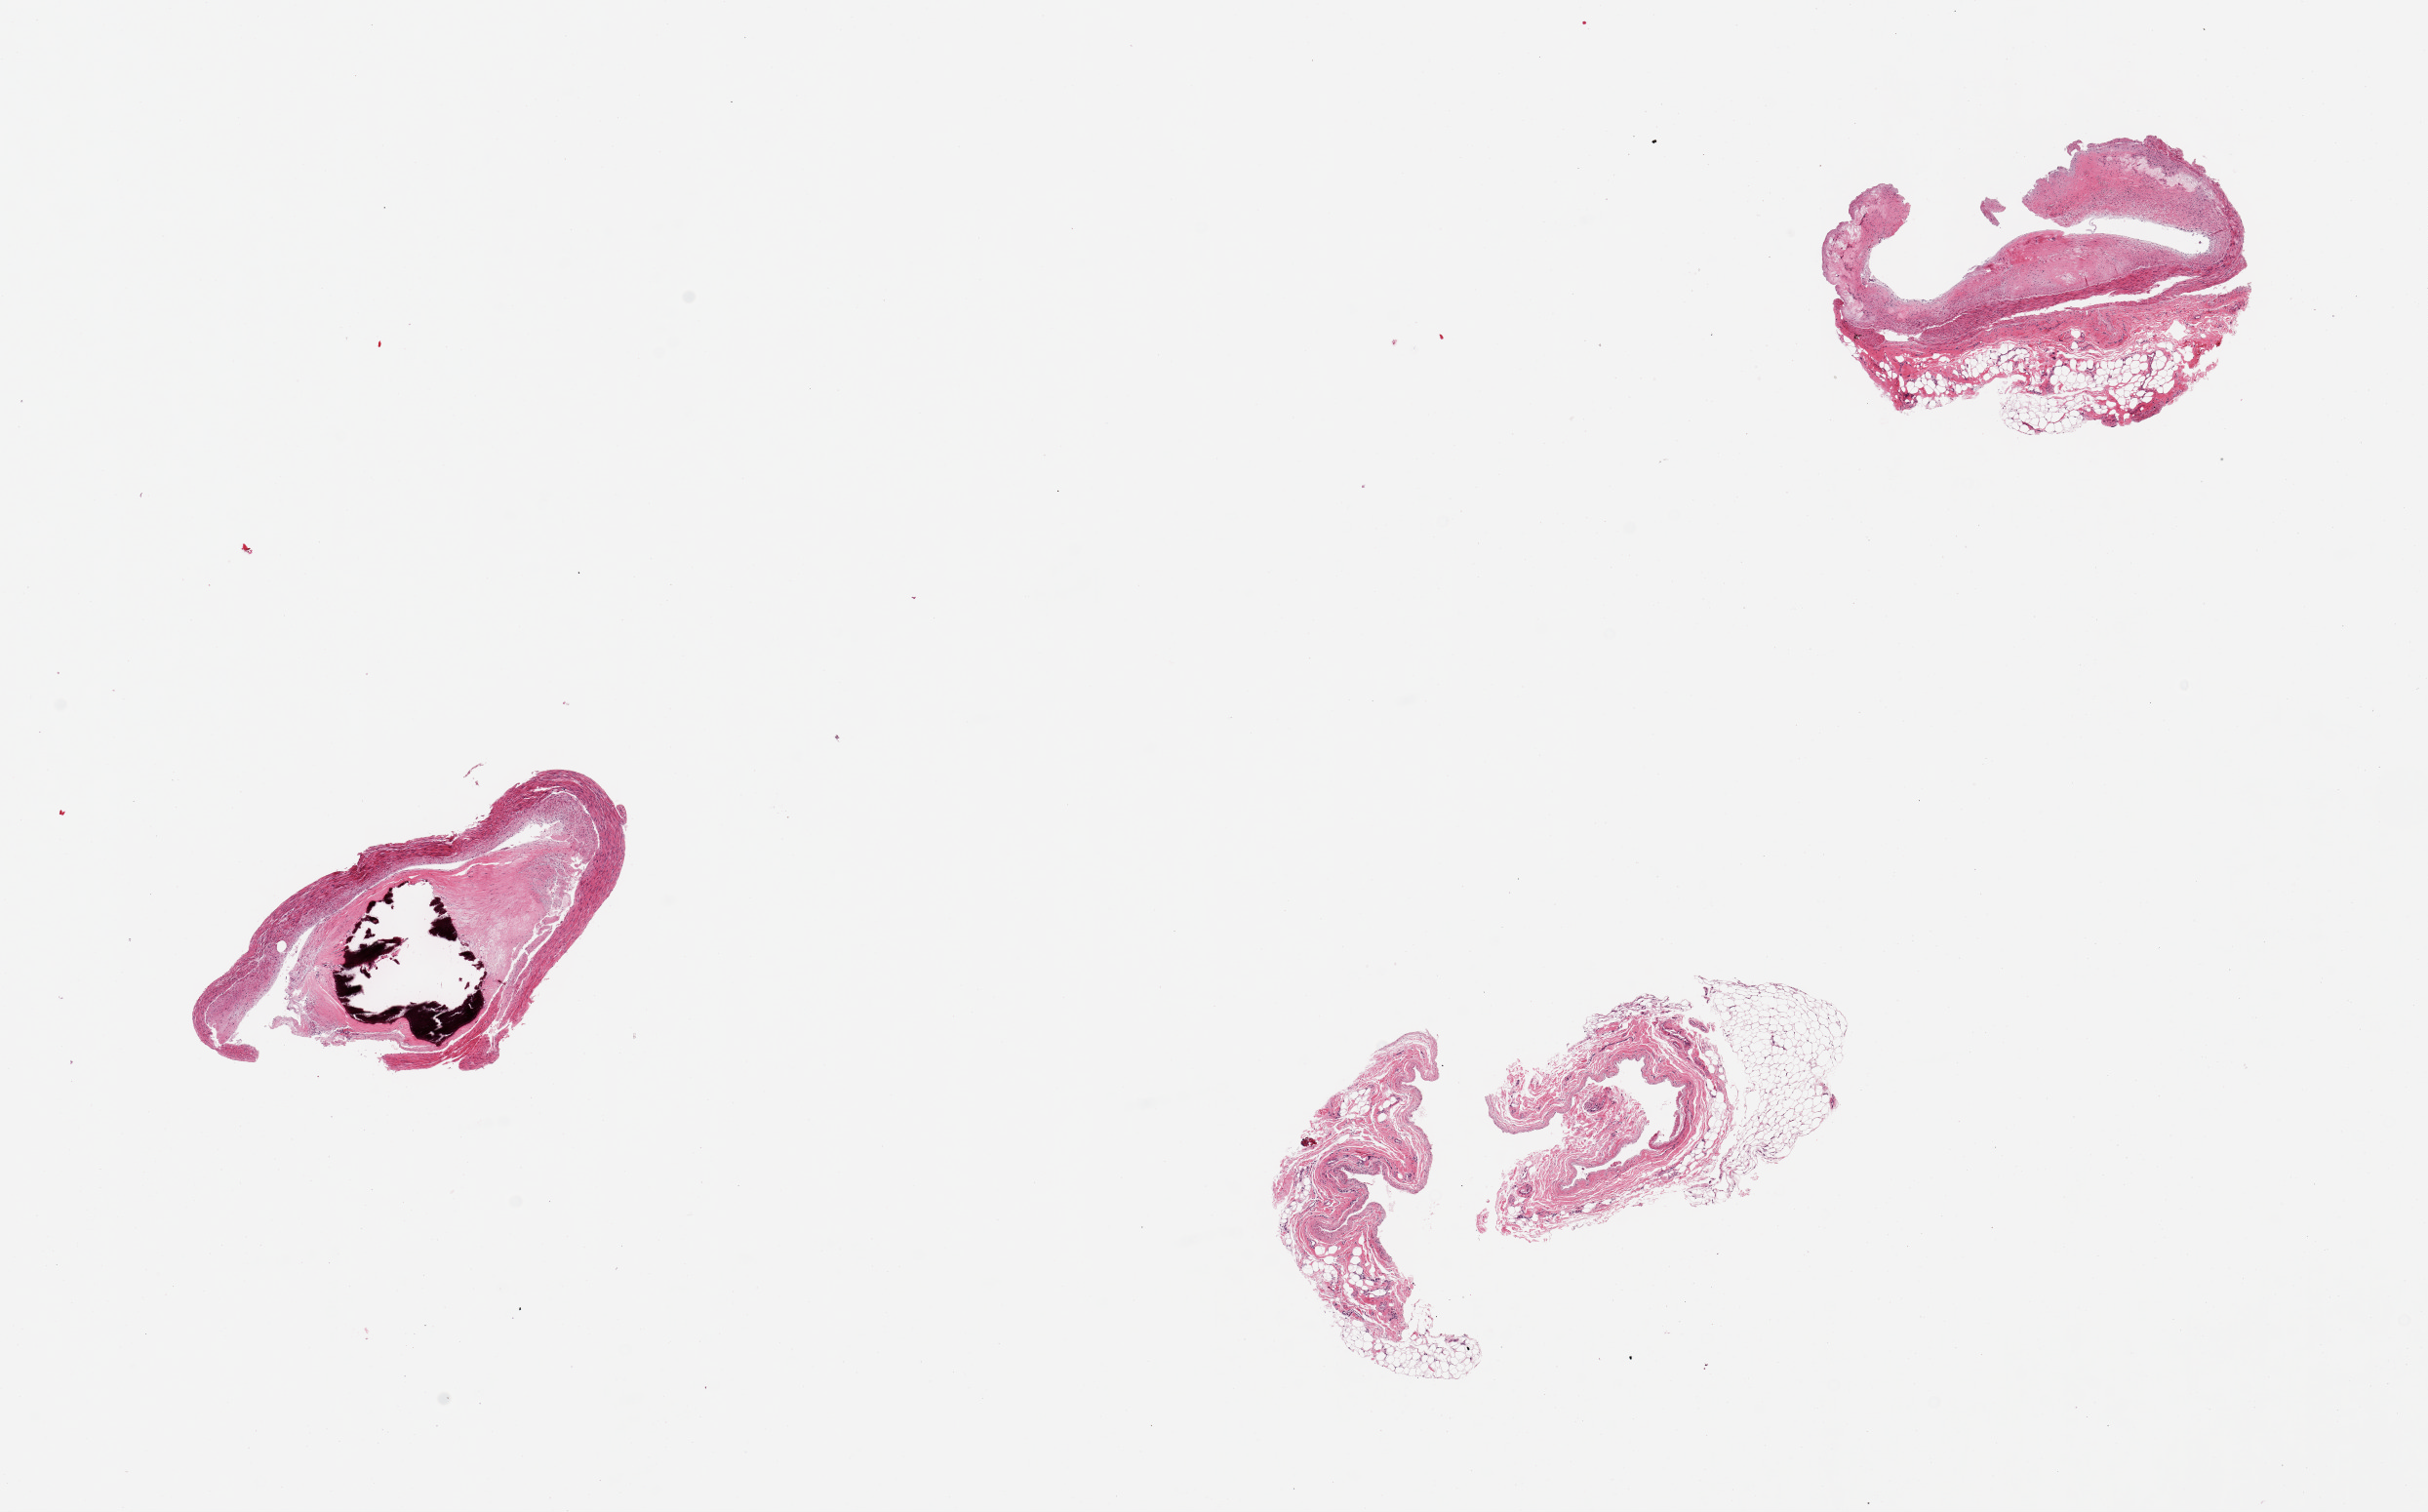
Whole-slide image, H&E stain, a low-resolution overview of the entire scanned area, about 19.7 x 12.3 mm (from a 20x scan), PAXgene-fixed, paraffin-embedded tissue, section of coronary artery (target tissue), tissue donor sample. Donor sex: male.
* reviewer comment on this tissue sample: 3 pieces; 2 fragments of artery with severe calcific atherosclerosis, unable to specify compromise of lumen due to fragmentation. Some residual attached adipose tissue and fragments of disrupted vessel and fat